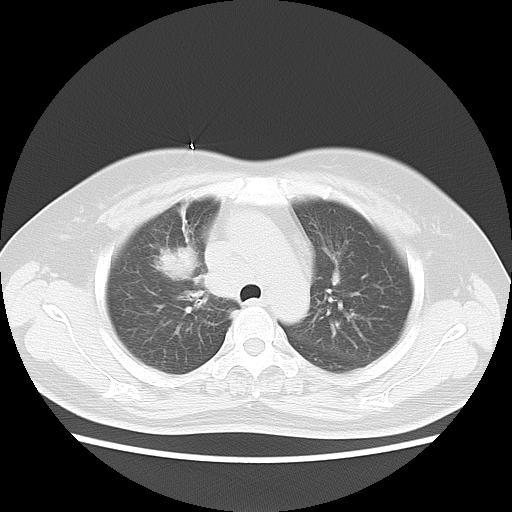
Chest CT, one axial slice; slice 11 of 18 in the series (ordered by position); reconstruction kernel LUNG; 120 kVp; lung window (W 1500 / L -600 HU); 5 mm slice thickness; 512 × 512 image matrix, field of view 350 × 350 mm. Female patient, age 54 years. From the clinical record (not read from this slice): clinical TNM (as recorded): T2 N3 M0.
Structures marked on this image (bounding box drawn by a radiologist):
- lung tumour (recorded histology: small cell carcinoma): box from (x=147, y=242) to (x=200, y=298) px